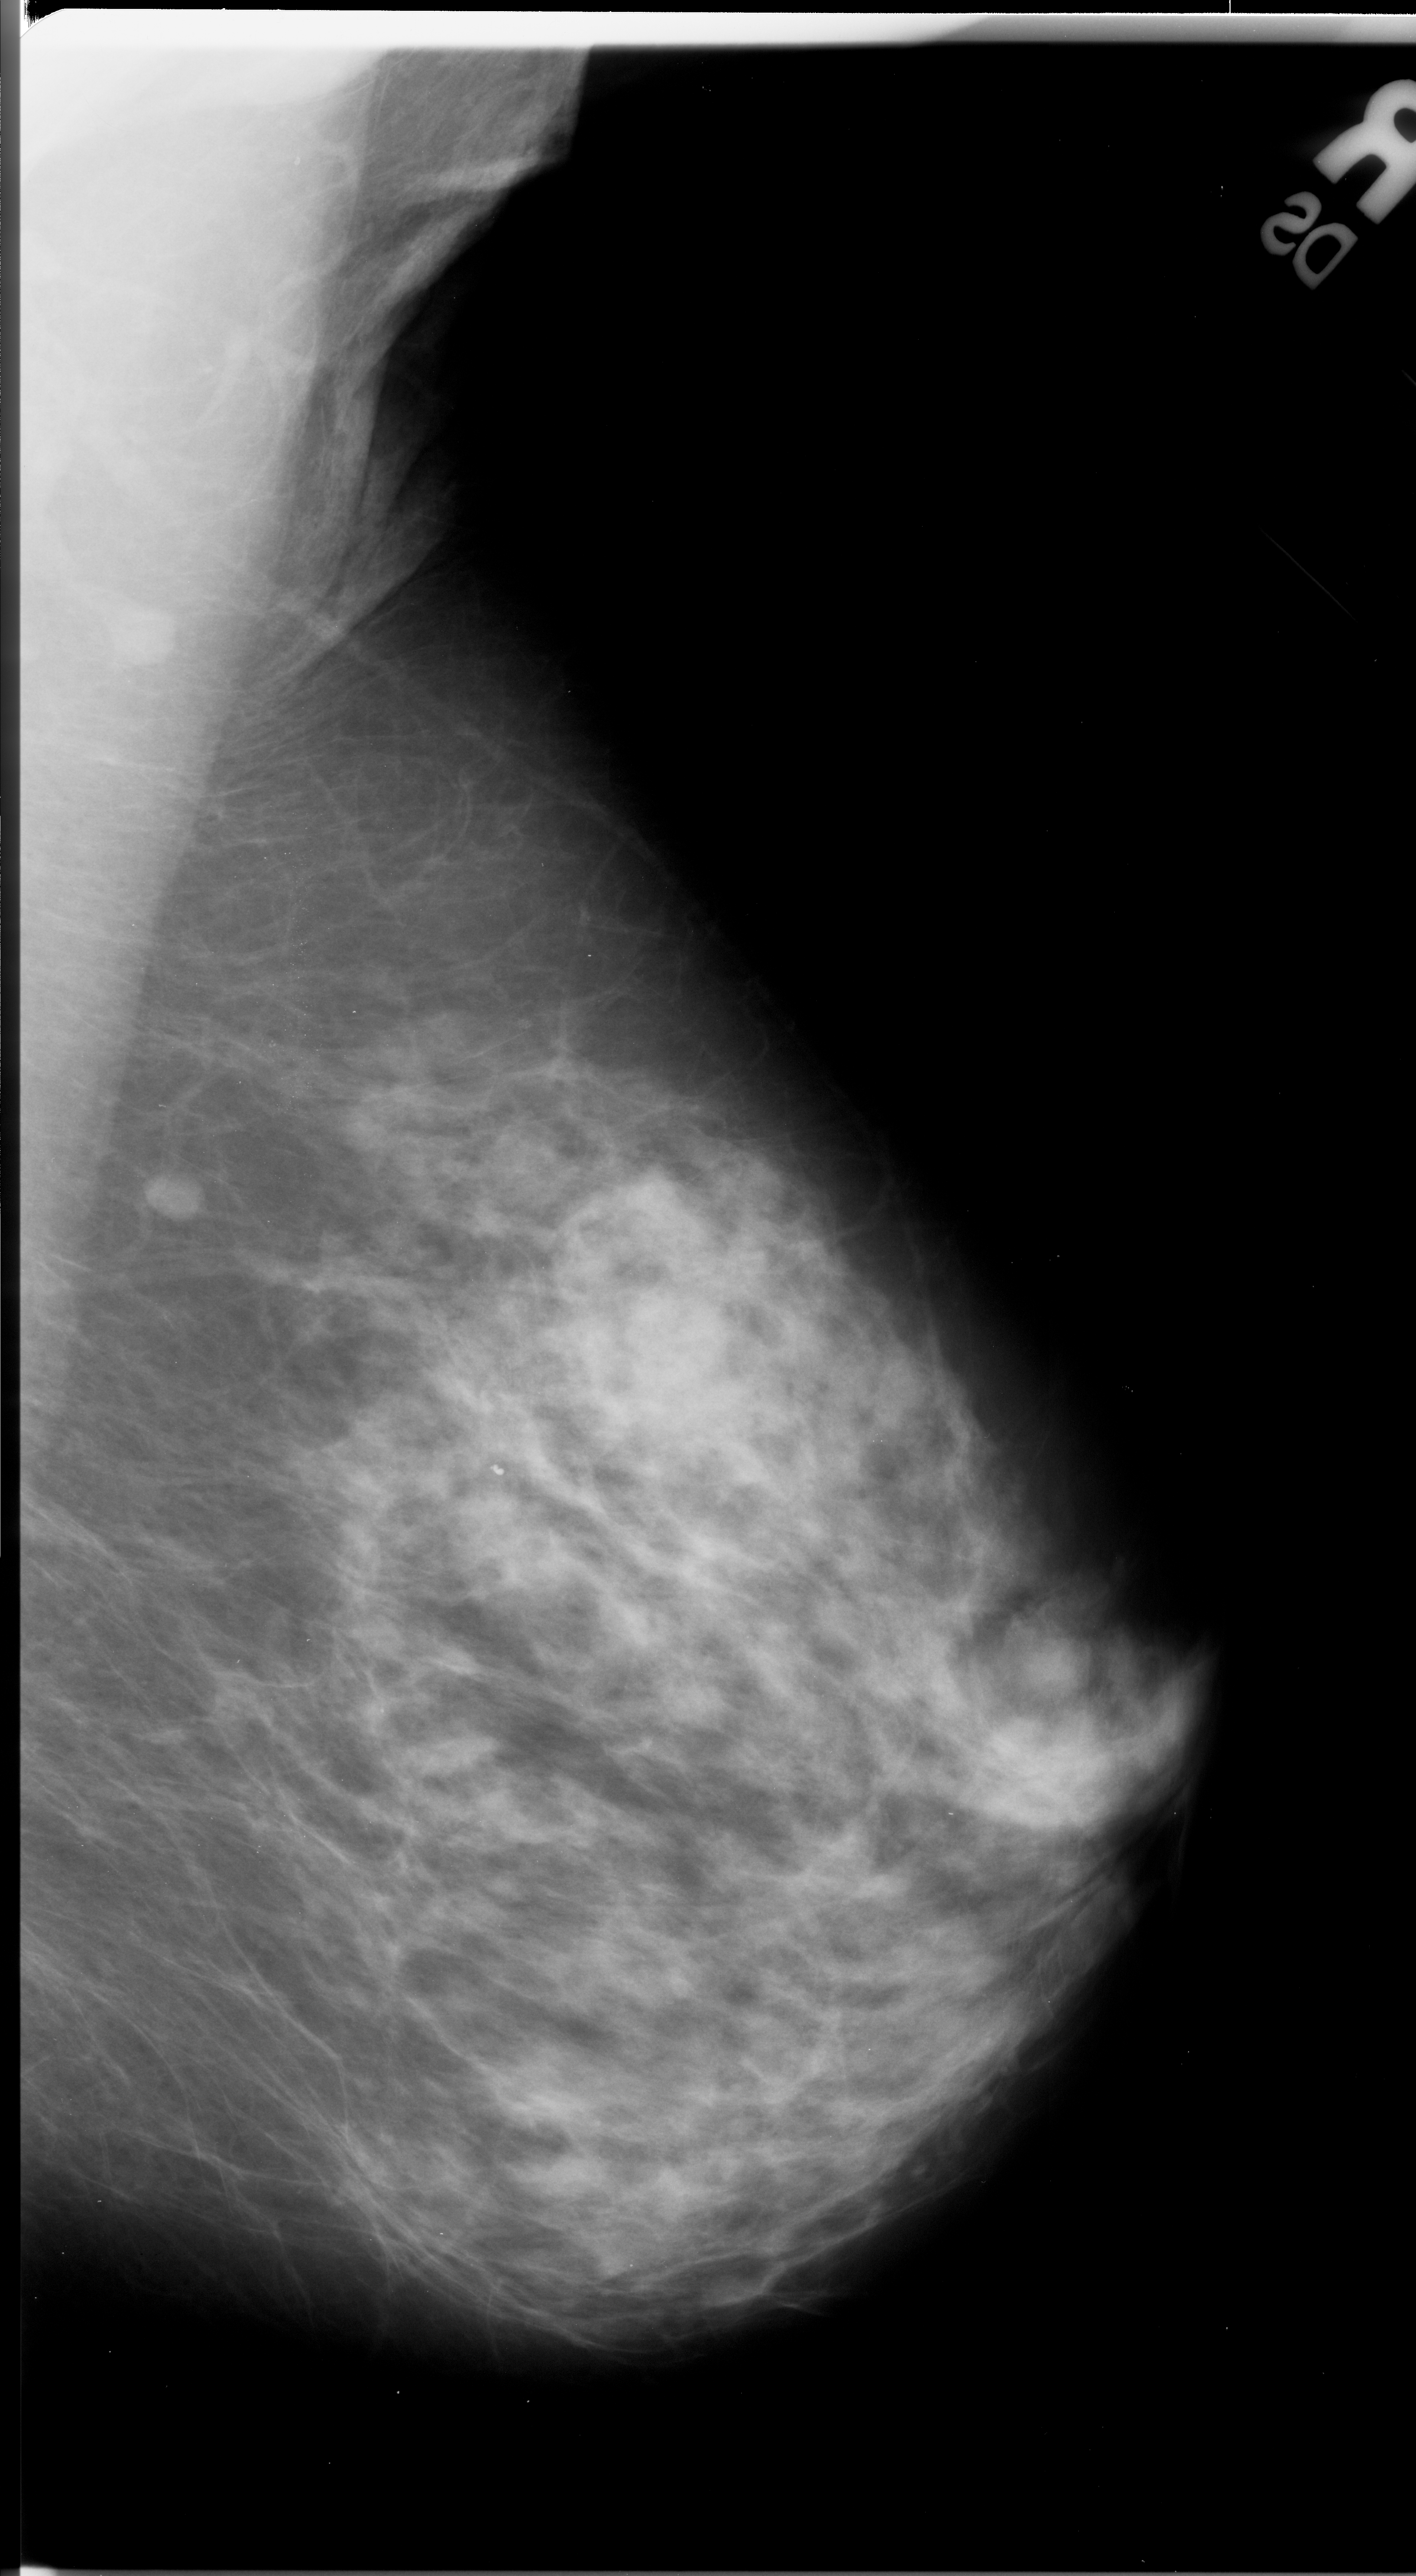
Scanned film-screen mammogram, right breast, mediolateral oblique (MLO) view, BI-RADS breast density category 3 (scale 1–4).
Finding: mass, shape architectural distortion, margins spiculated; BI-RADS assessment category 5; pathology (as recorded): malignant.